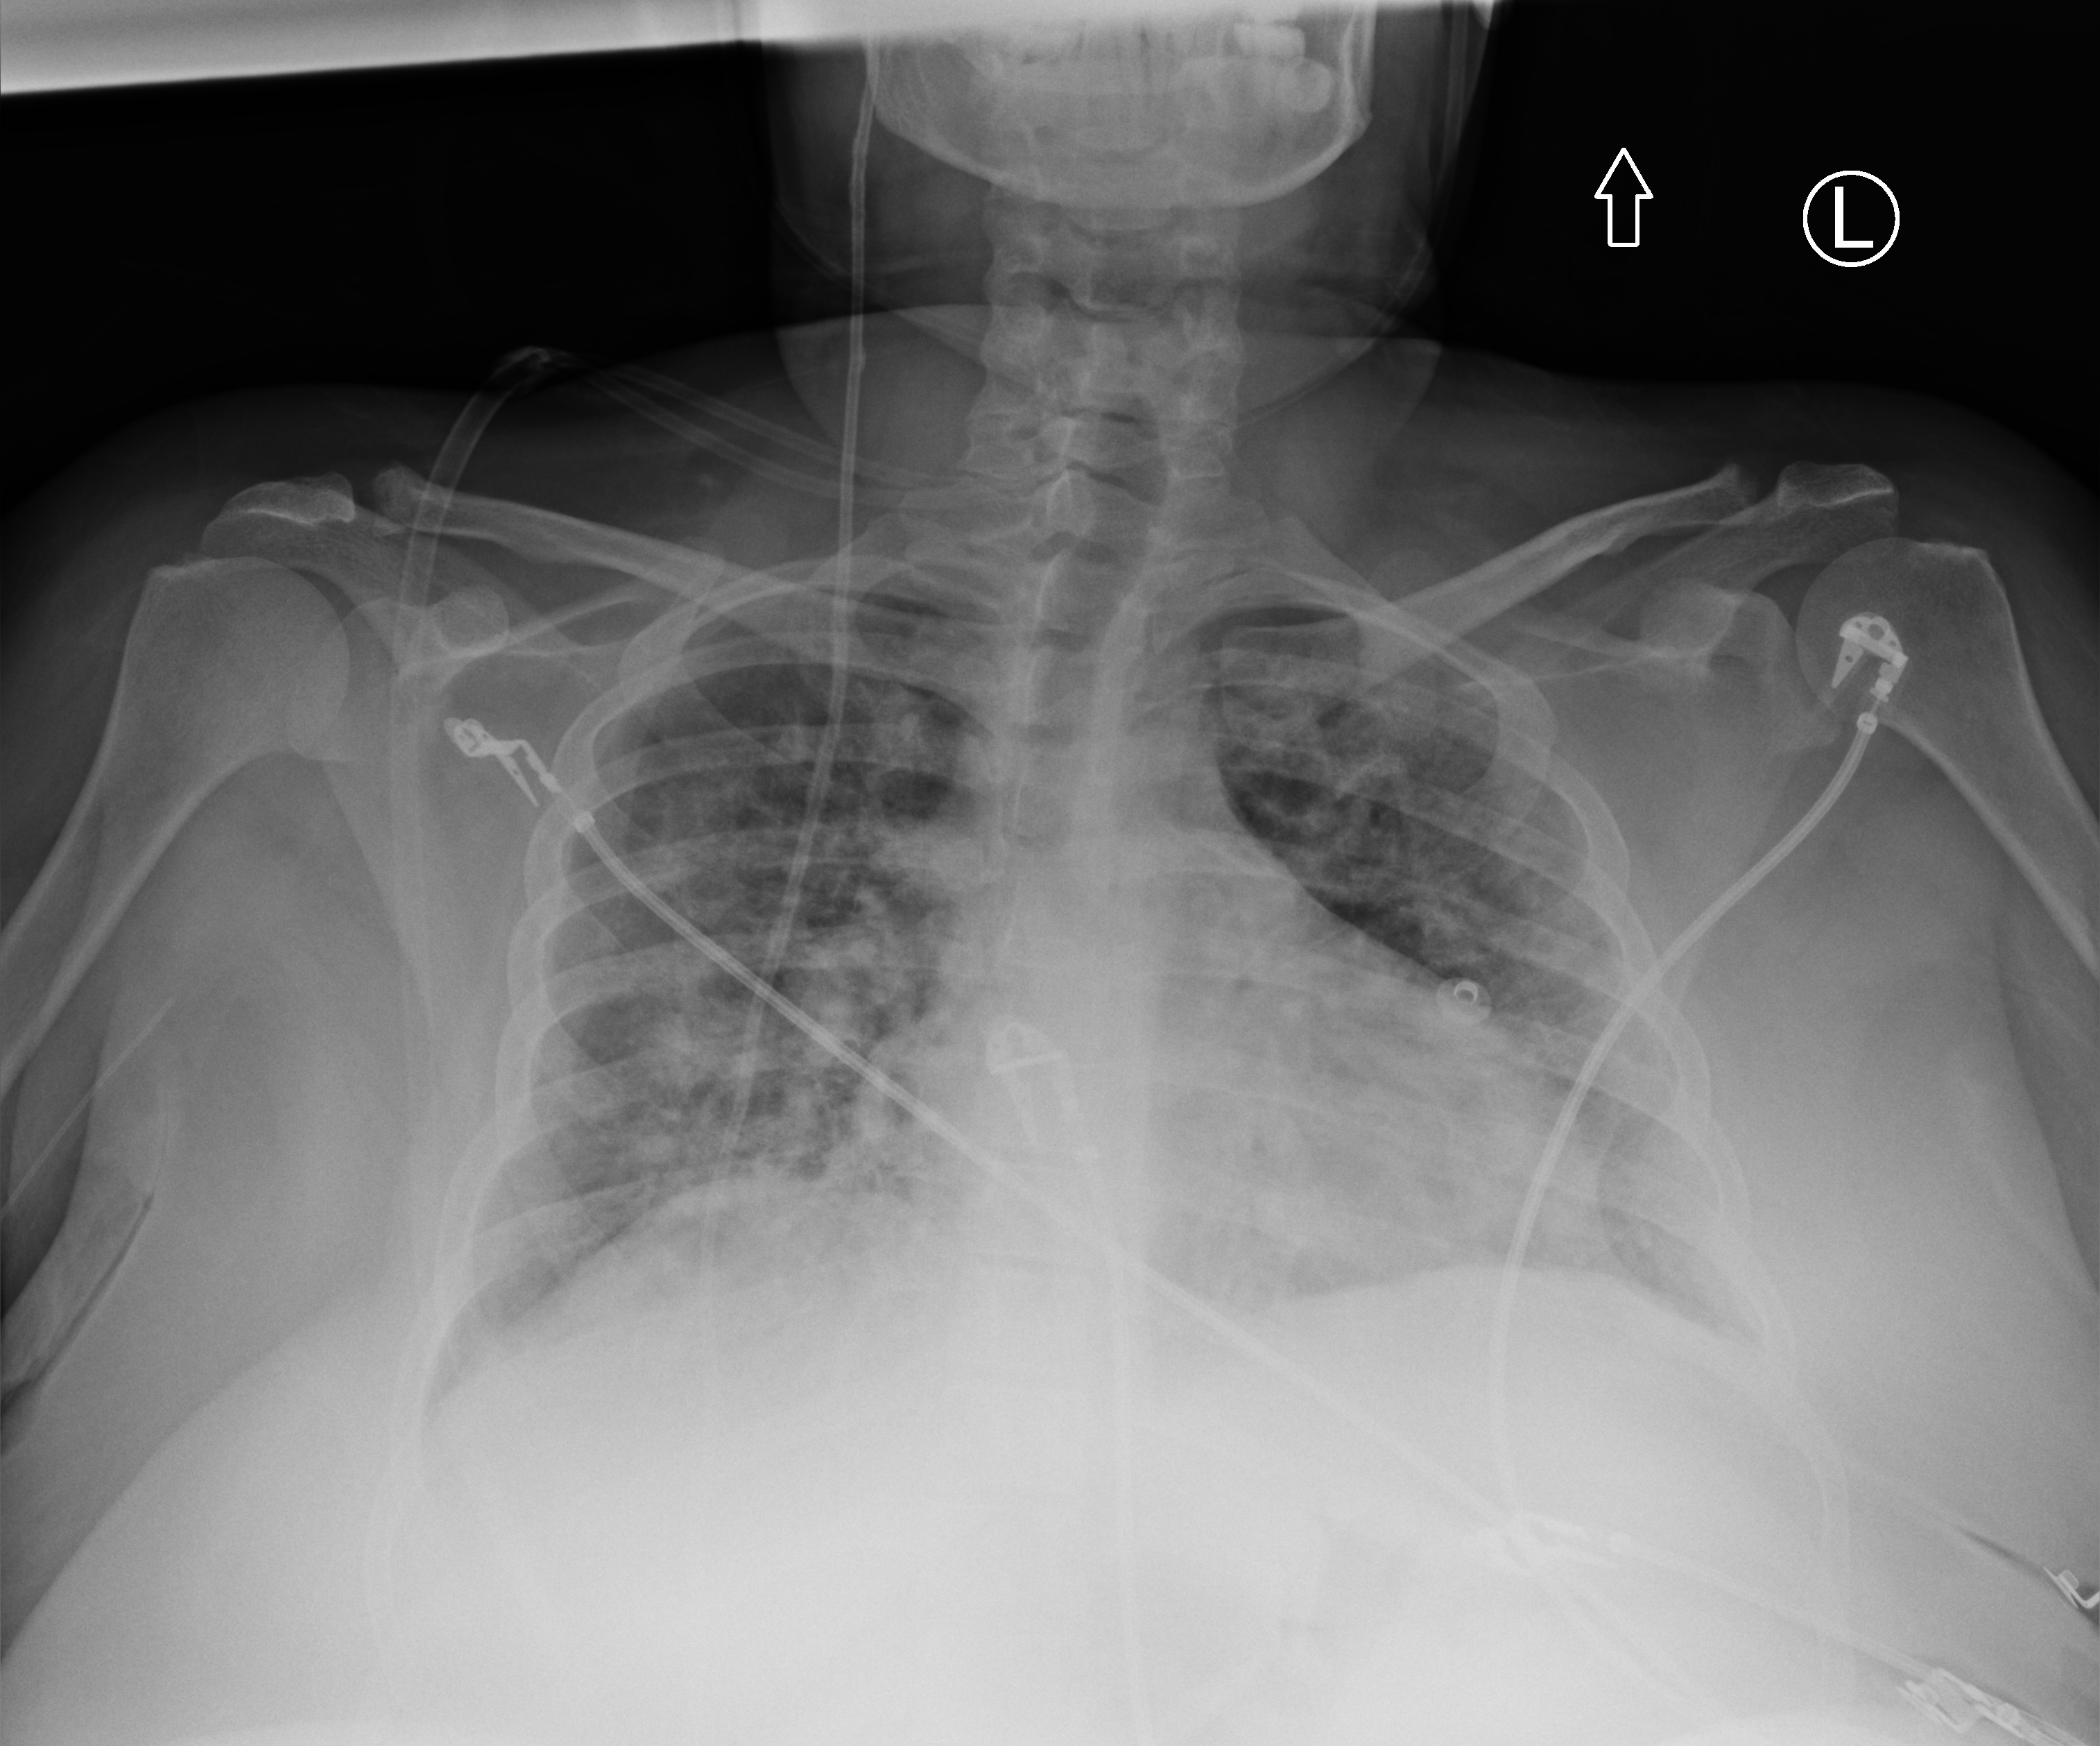
Bedside chest radiograph (computed radiography). Patient hospitalised with COVID-19; female, aged 18–59 years.
Admission-level facts for this patient (not findings on this image; timing relative to this image not recorded): admitted to intensive care during this hospital stay: no.